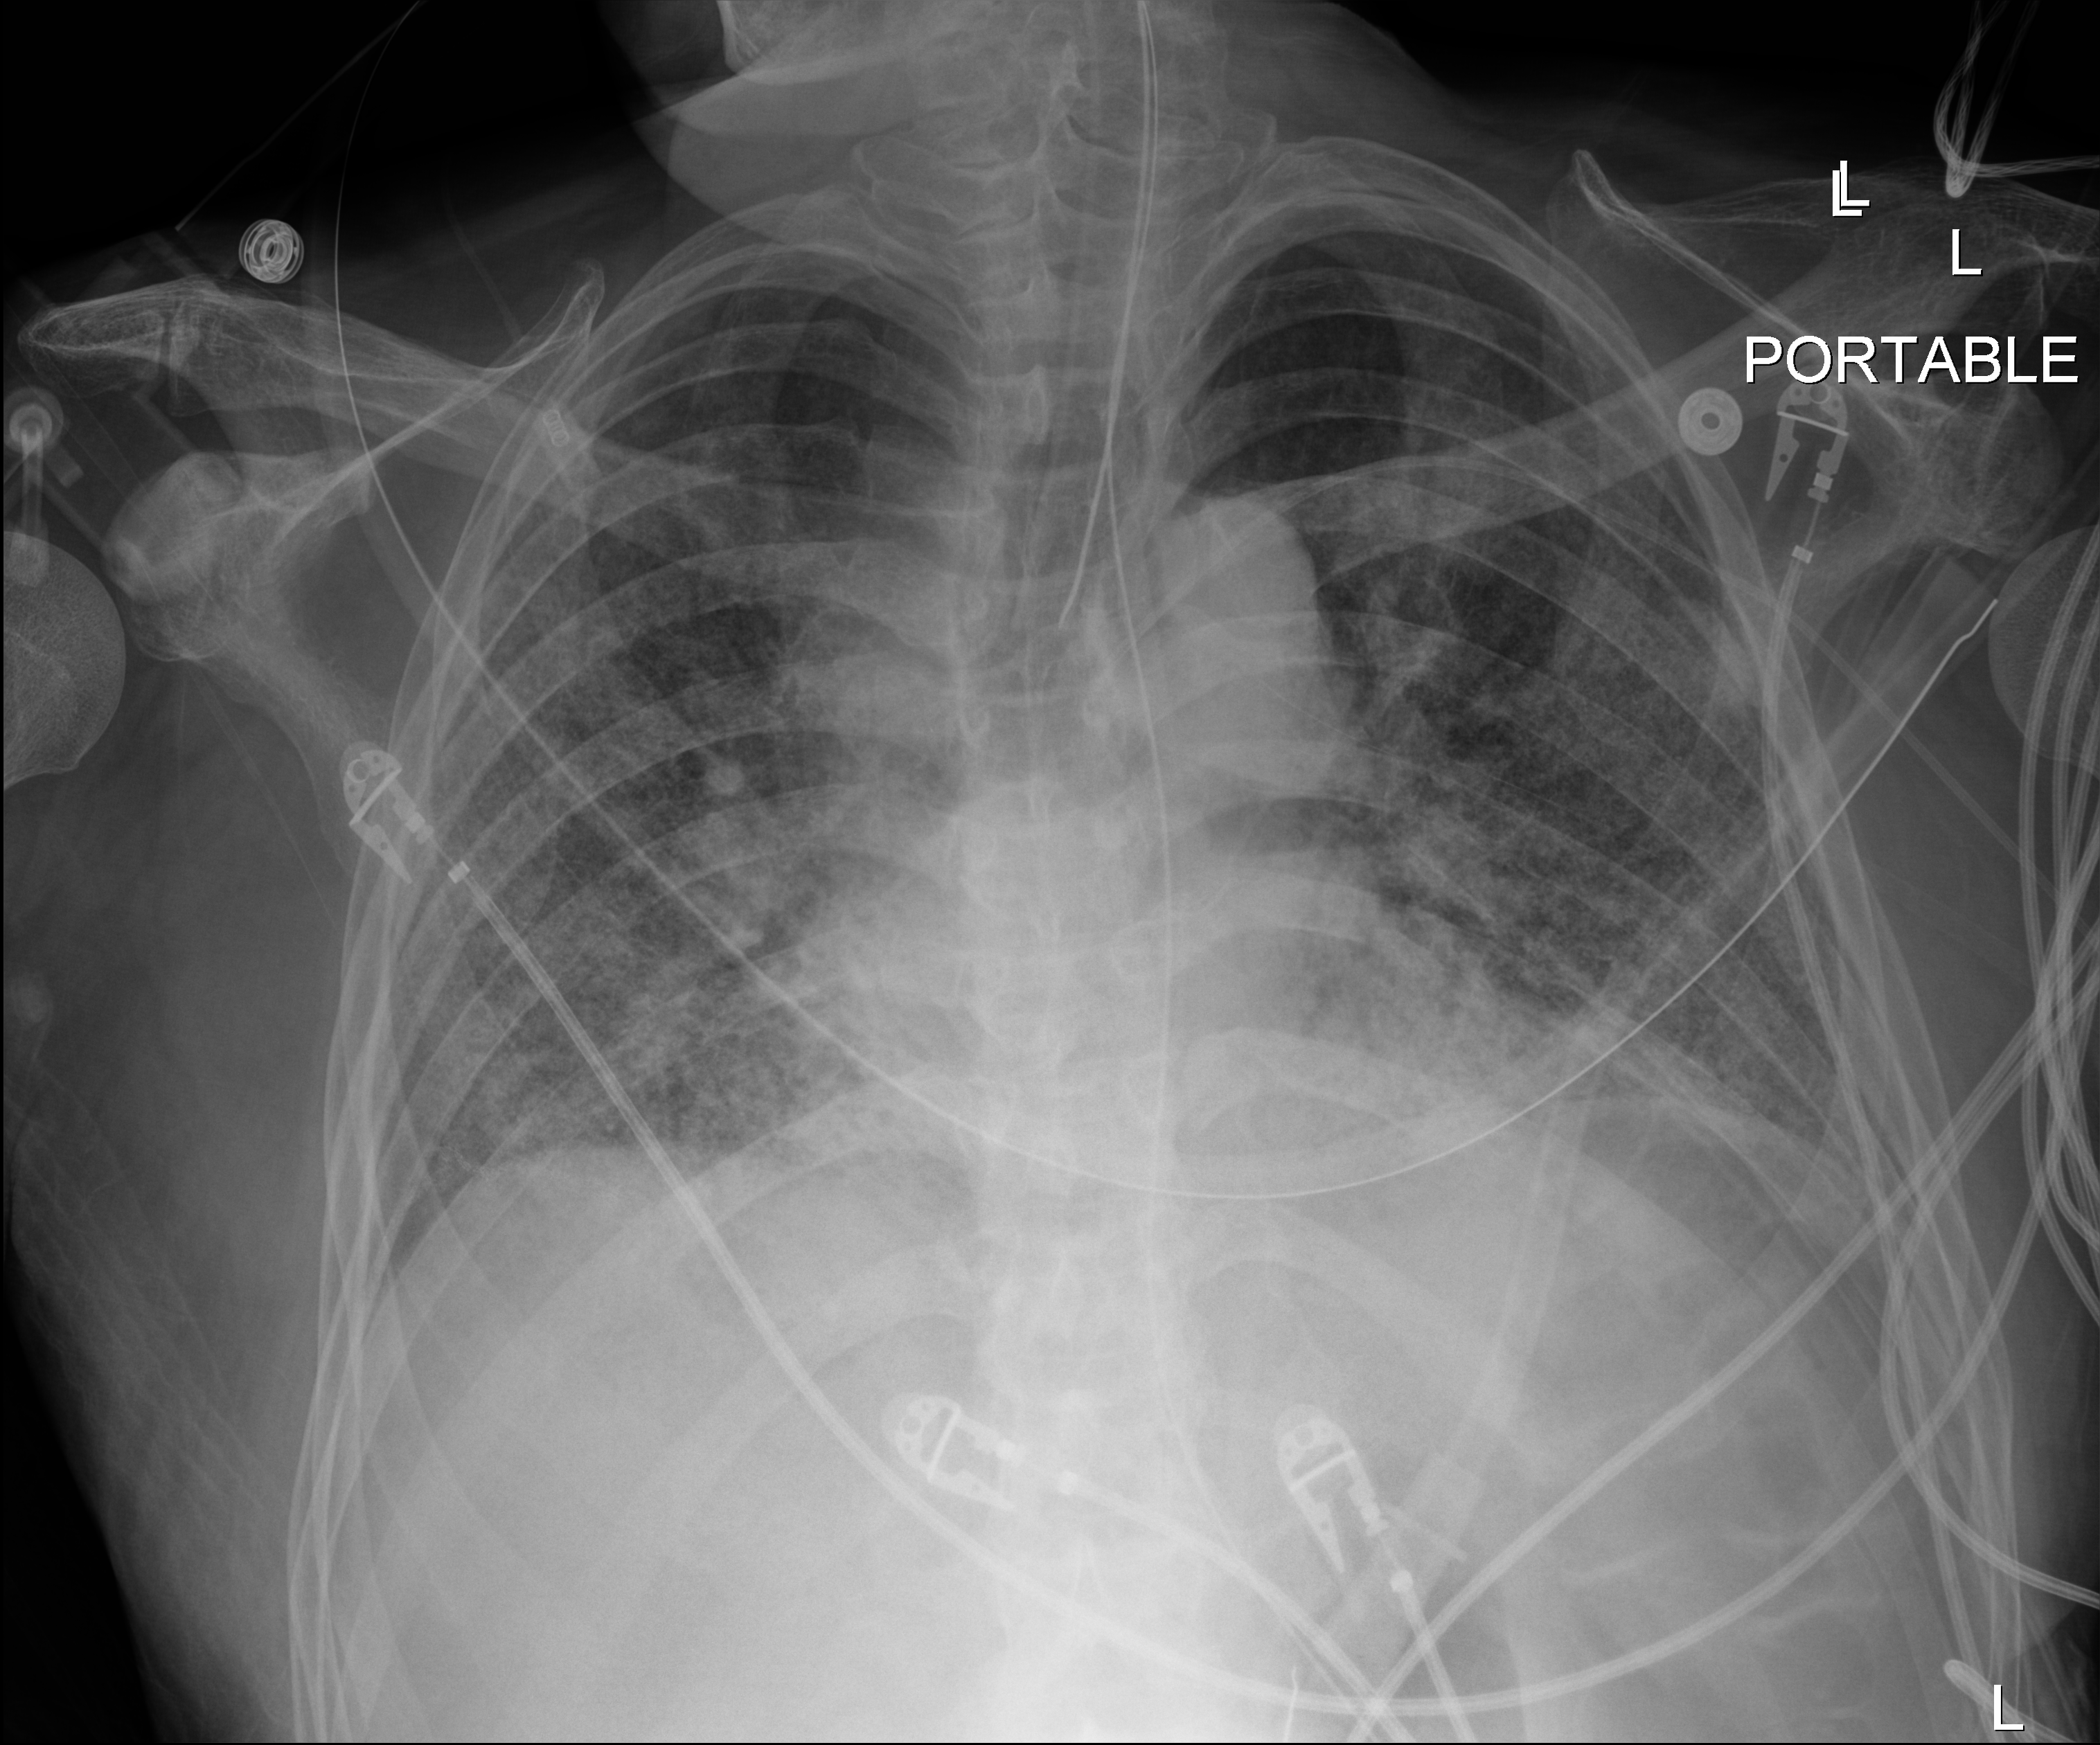
Chest radiograph, anteroposterior (AP) projection. Patient hospitalised with COVID-19; male, aged 60–74 years.
From the hospital-stay record, not from the radiograph (when in the stay this image was taken is not recorded): admitted to intensive care during this hospital stay: yes; mechanically ventilated during this hospital stay: yes.